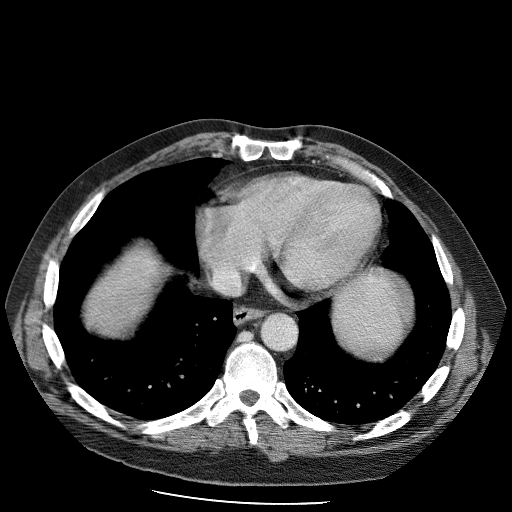
Contrast-enhanced abdominal CT (liver protocol), one axial slice; slice 96 of 98 in the series (ordered by position); 120 kVp; soft-tissue window (W 400 / L 40 HU); 2.5 mm slice thickness; 512 × 512 image matrix. Case-level facts recorded for this patient, not image findings: diagnosis: hepatocellular carcinoma (patient treated with transarterial chemoembolisation; whether this scan precedes or follows treatment is not stated here); TNM stage (as recorded): Stage-II; Child-Pugh class: B; tumour differentiation: moderately differentiated; tumour nodularity: uninodular.
Outlined on this slice (semi-automatically segmented with operator editing):
- liver parenchyma outside the tumour (the mass and vessels are separate outlines, so this box may not span the whole liver): bounding box <86,248,158,326> (left, top, right, bottom; pixels)